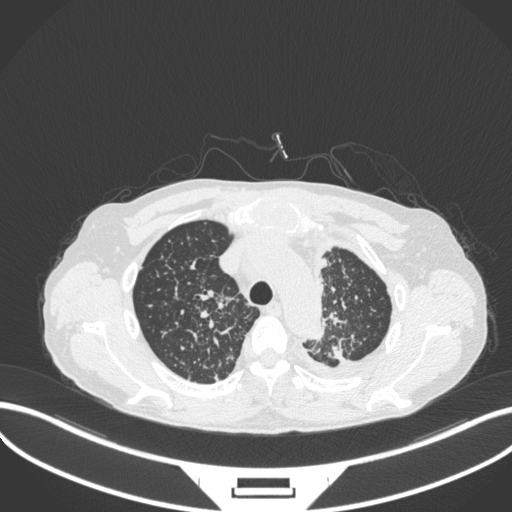
Chest CT, one axial slice; position 277 of 319 along the scan axis; lung window (W 1500 / L -600 HU); 512 × 512 image matrix. Male patient, age 58 years. Case-level facts recorded for this patient, not image findings: clinical TNM (as recorded): T1c N3 M1.
Annotated regions visible in this slice (rectangle marked by the reading radiologist):
- lung tumour (recorded histology: adenocarcinoma): bounding box [x1, y1, x2, y2] px = [322, 338, 353, 364]